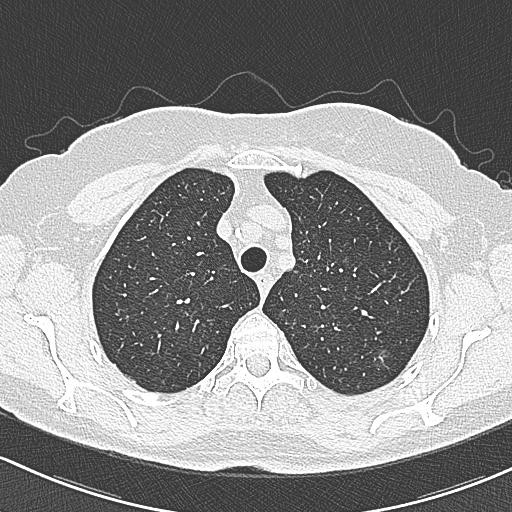
Axial slice from a low-dose chest CT screening exam, baseline screening round, lung window (W 1500 / L -600 HU), slice 60 of 312 in the series, 512 × 512 image matrix, field of view 318 × 318 mm. Female participant, aged 65 years at enrolment. Current smoker at enrolment.
- Expert reader's lesion annotation, bounding box [x1, y1, x2, y2] px = [368, 346, 403, 380].
- The screening reader recorded 3 non-calcified nodules or masses ≥4 mm on this exam (left upper lobe, left upper lobe, right upper lobe); which of them this box marks is not recorded.